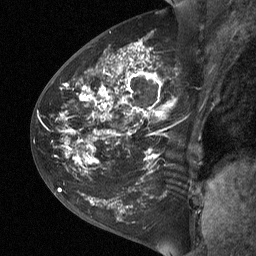
Breast MRI (dynamic contrast-enhanced), one sagittal slice. Dynamic contrast-enhanced study with each time point stored as its own series, time point 2 of 3 at this slice position (early post-contrast, ordered by acquisition time). 1.5 T. TE 4.8 ms, TR 27 ms. 2 mm slice thickness. 256 × 256 image matrix, field of view 200 × 200 mm. Female patient, age 42 years. Case-level facts recorded for this patient, not image findings: setting: breast cancer imaged before/during neoadjuvant chemotherapy; receptor status: triple-negative.
Outlined on this slice (semi-automatically segmented with operator editing):
- analysis volume of interest (the breast-tissue region the enhancement analysis was run in; not a lesion): bounding box (x1, y1, x2, y2) in pixels: (43, 29, 194, 190)
- tumour enhancement mask (voxels above the 90 % enhancement threshold inside the analysis volume of interest): (65, 47, 162, 164)